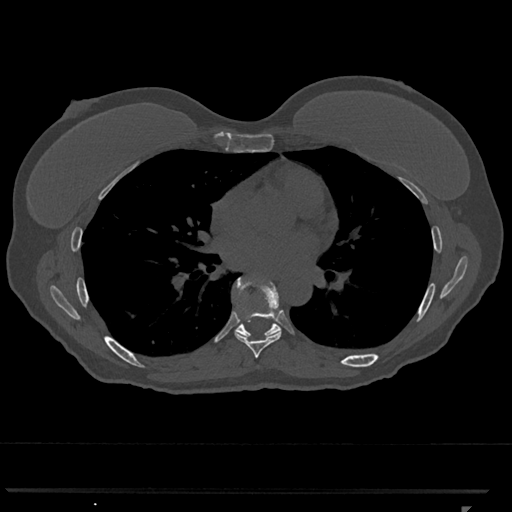
CT including the spine, one axial slice; position 696 of 793 along the scan axis; reconstruction kernel Br40s/3; bone window (W 1800 / L 400 HU); 0.5 mm slice thickness; 512 × 512 image matrix, field of view 380 × 380 mm. Patient: female, 62 years. Case-level facts recorded for this patient, not image findings: primary cancer: renal.
Structures marked on this image (semi-automatically segmented with operator editing):
- T7 vertebra: bounding box (x1, y1, x2, y2) in pixels: (234, 277, 282, 358)
- T8 vertebra: (234, 277, 281, 337)